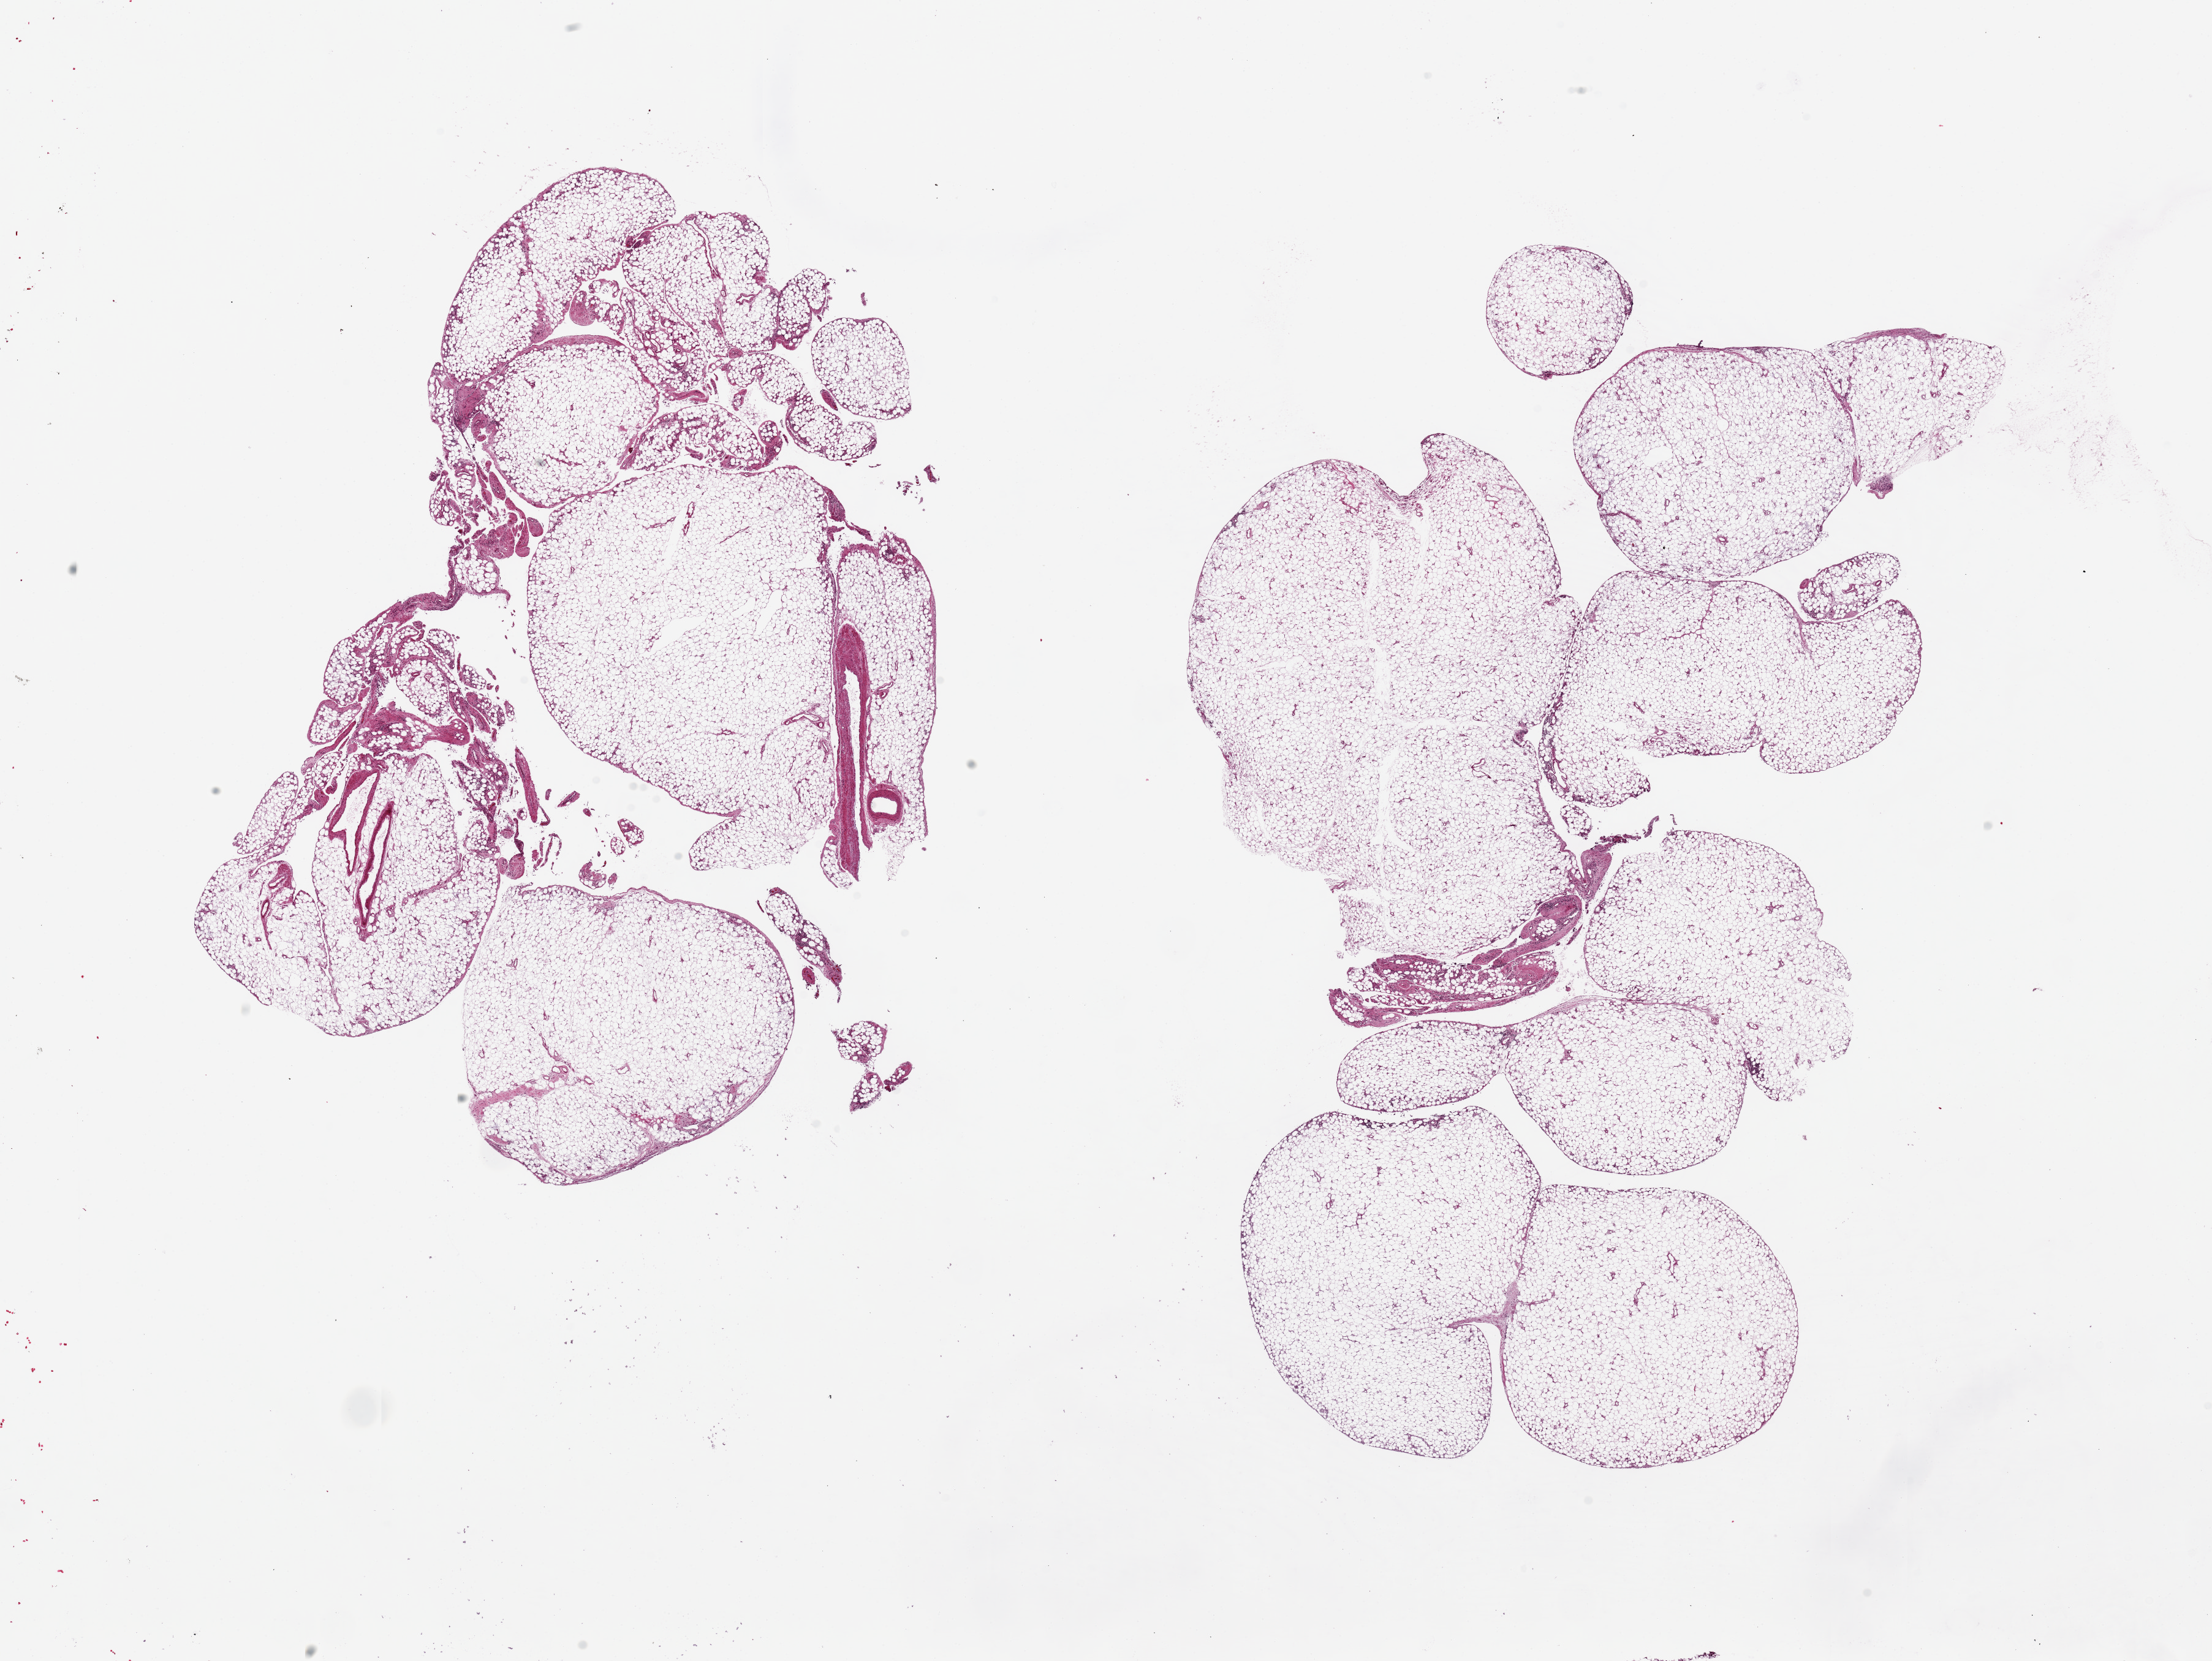
Whole-slide image, hematoxylin and eosin (H&E) stain — shown as a low-resolution overview of the whole scanned area (about 28.5 x 21.4 mm); PAXgene-fixed, paraffin-embedded tissue; sampled site (target tissue): omentum; donor tissue sample. Donor sex: female.
• pathologist's review note for this sample: 2 pieces, 13x10 & 16x10.5mm